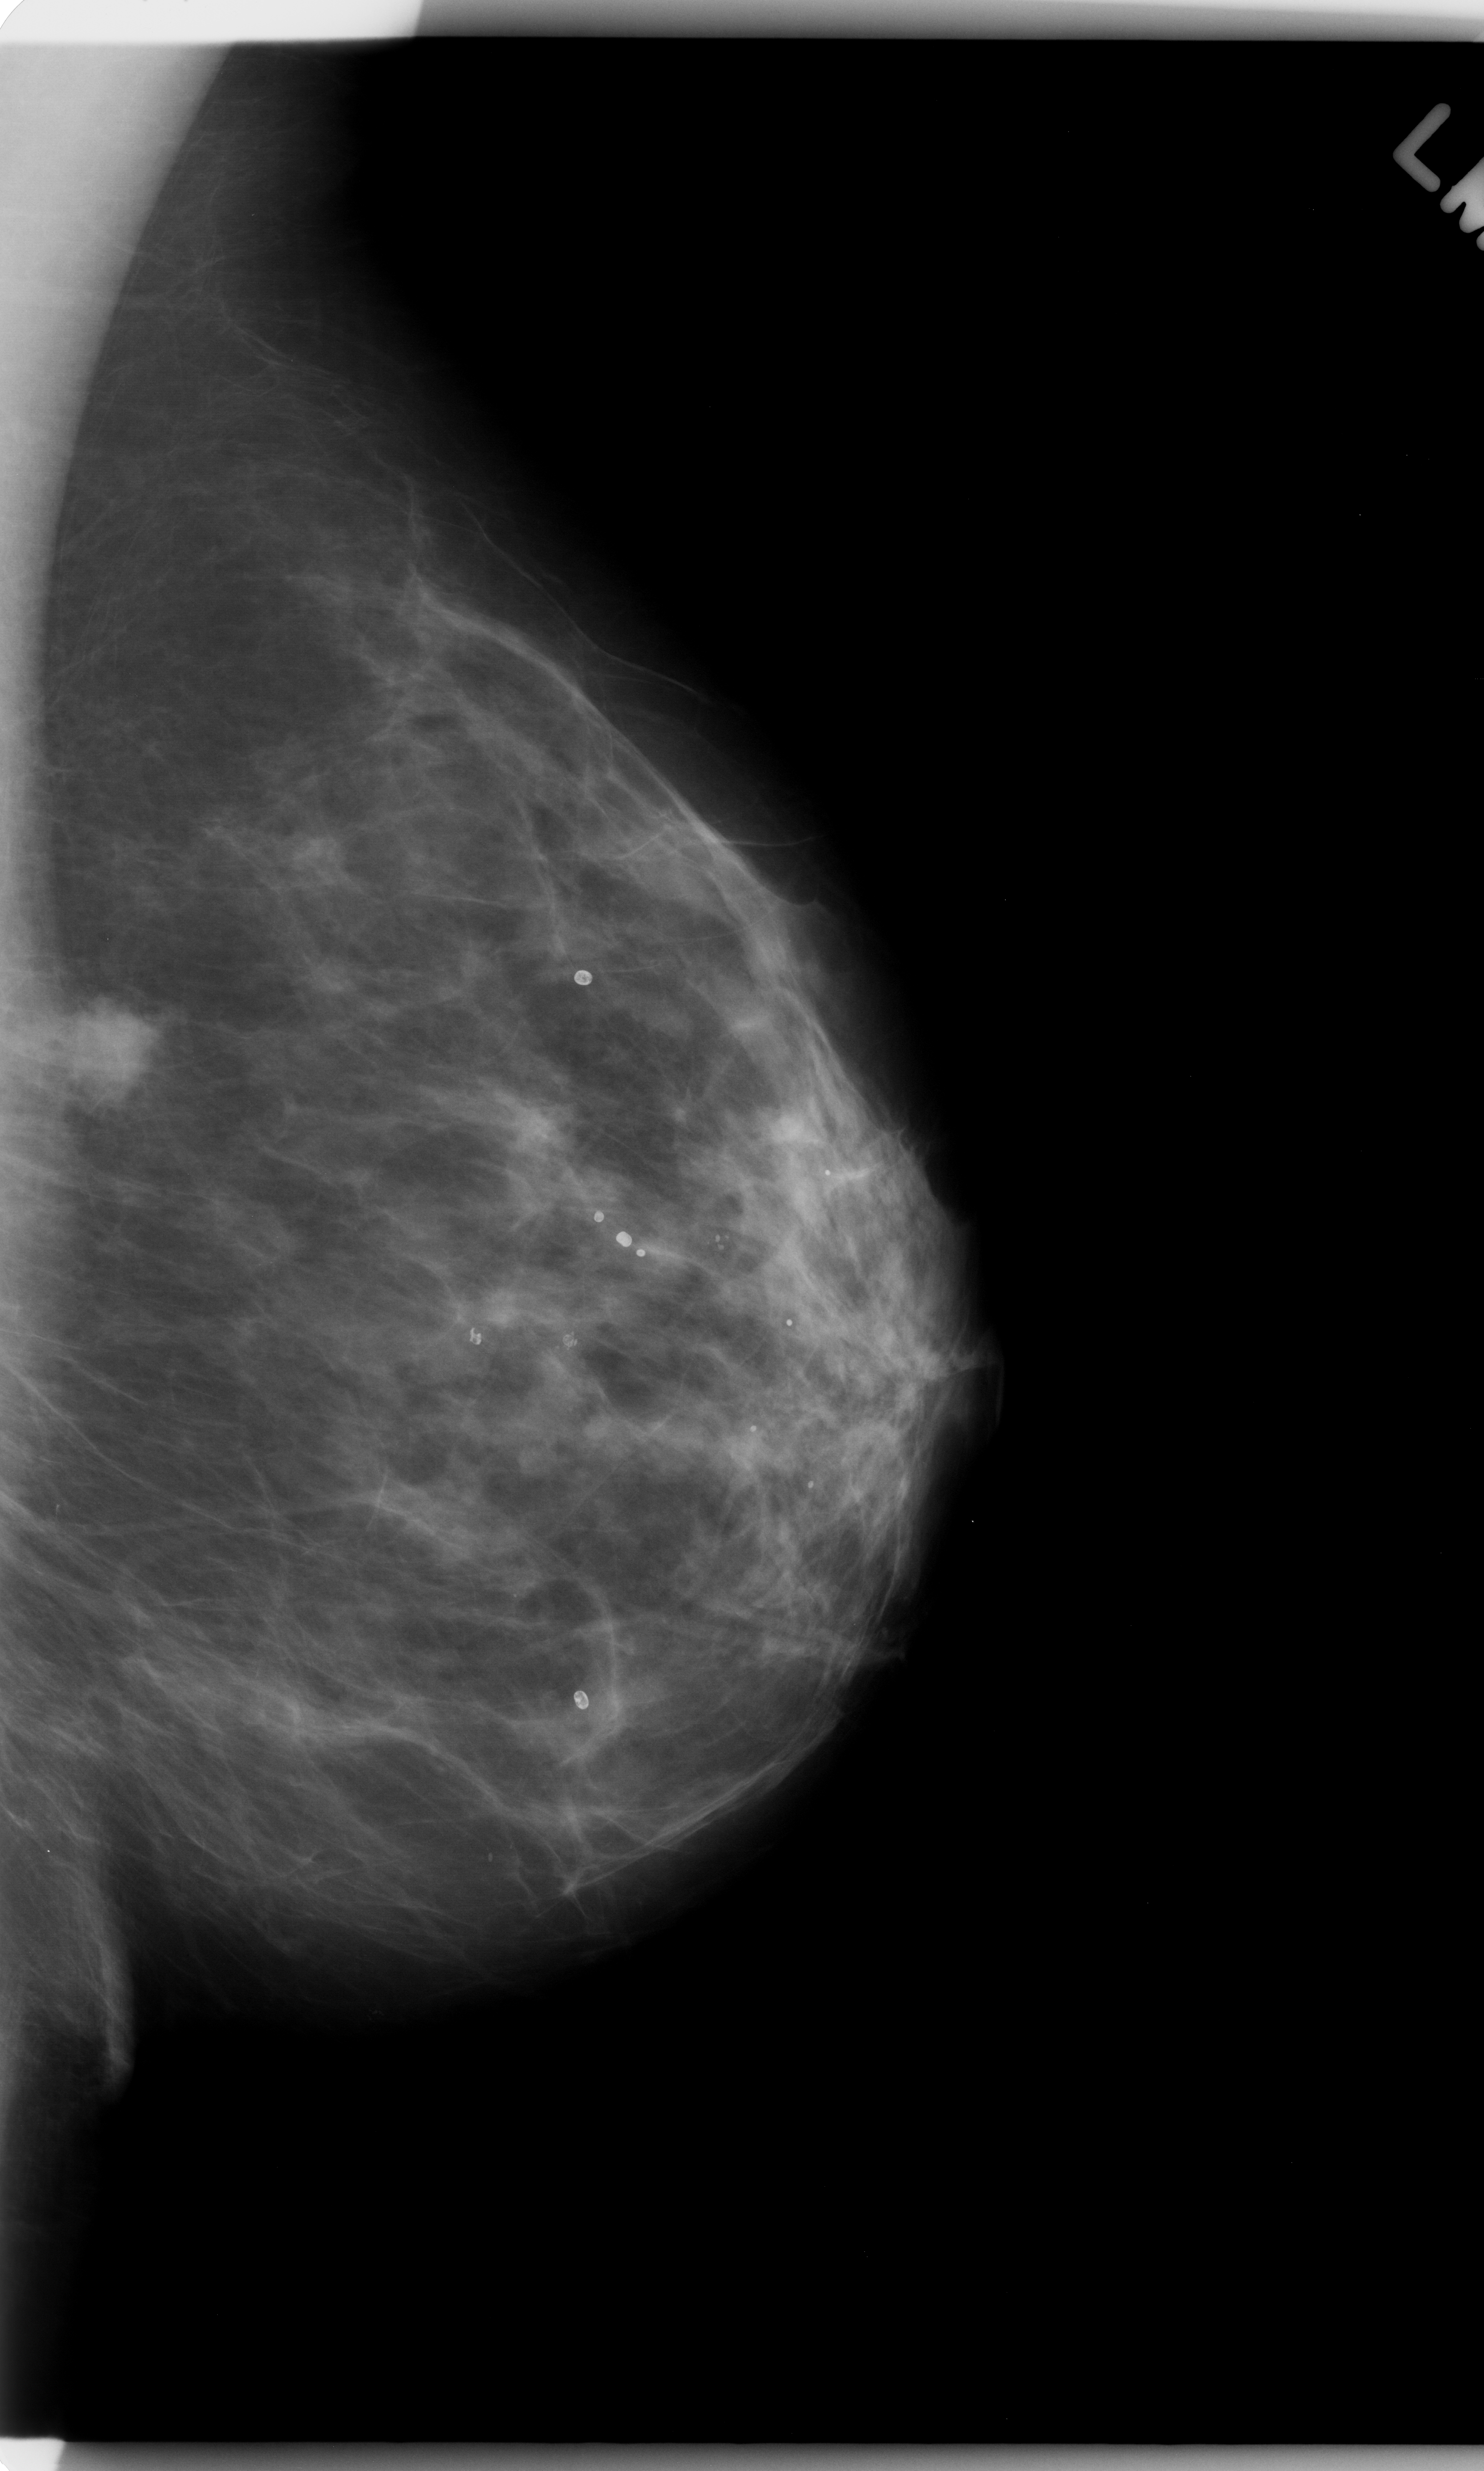
Mammogram (digitized film); left breast; mediolateral oblique (MLO) view; BI-RADS breast density category 2 (scale 1–4); 1484 × 2471 image matrix.
Expert-marked regions of interest on this film, with their recorded descriptors:
- mass, shape lobulated, margins microlobulated; BI-RADS assessment category 5; subtlety rating 5 on a 1 (subtle) to 5 (obvious) scale; pathology (as recorded): malignant: bounding box <32,992,178,1117> (left, top, right, bottom; pixels)